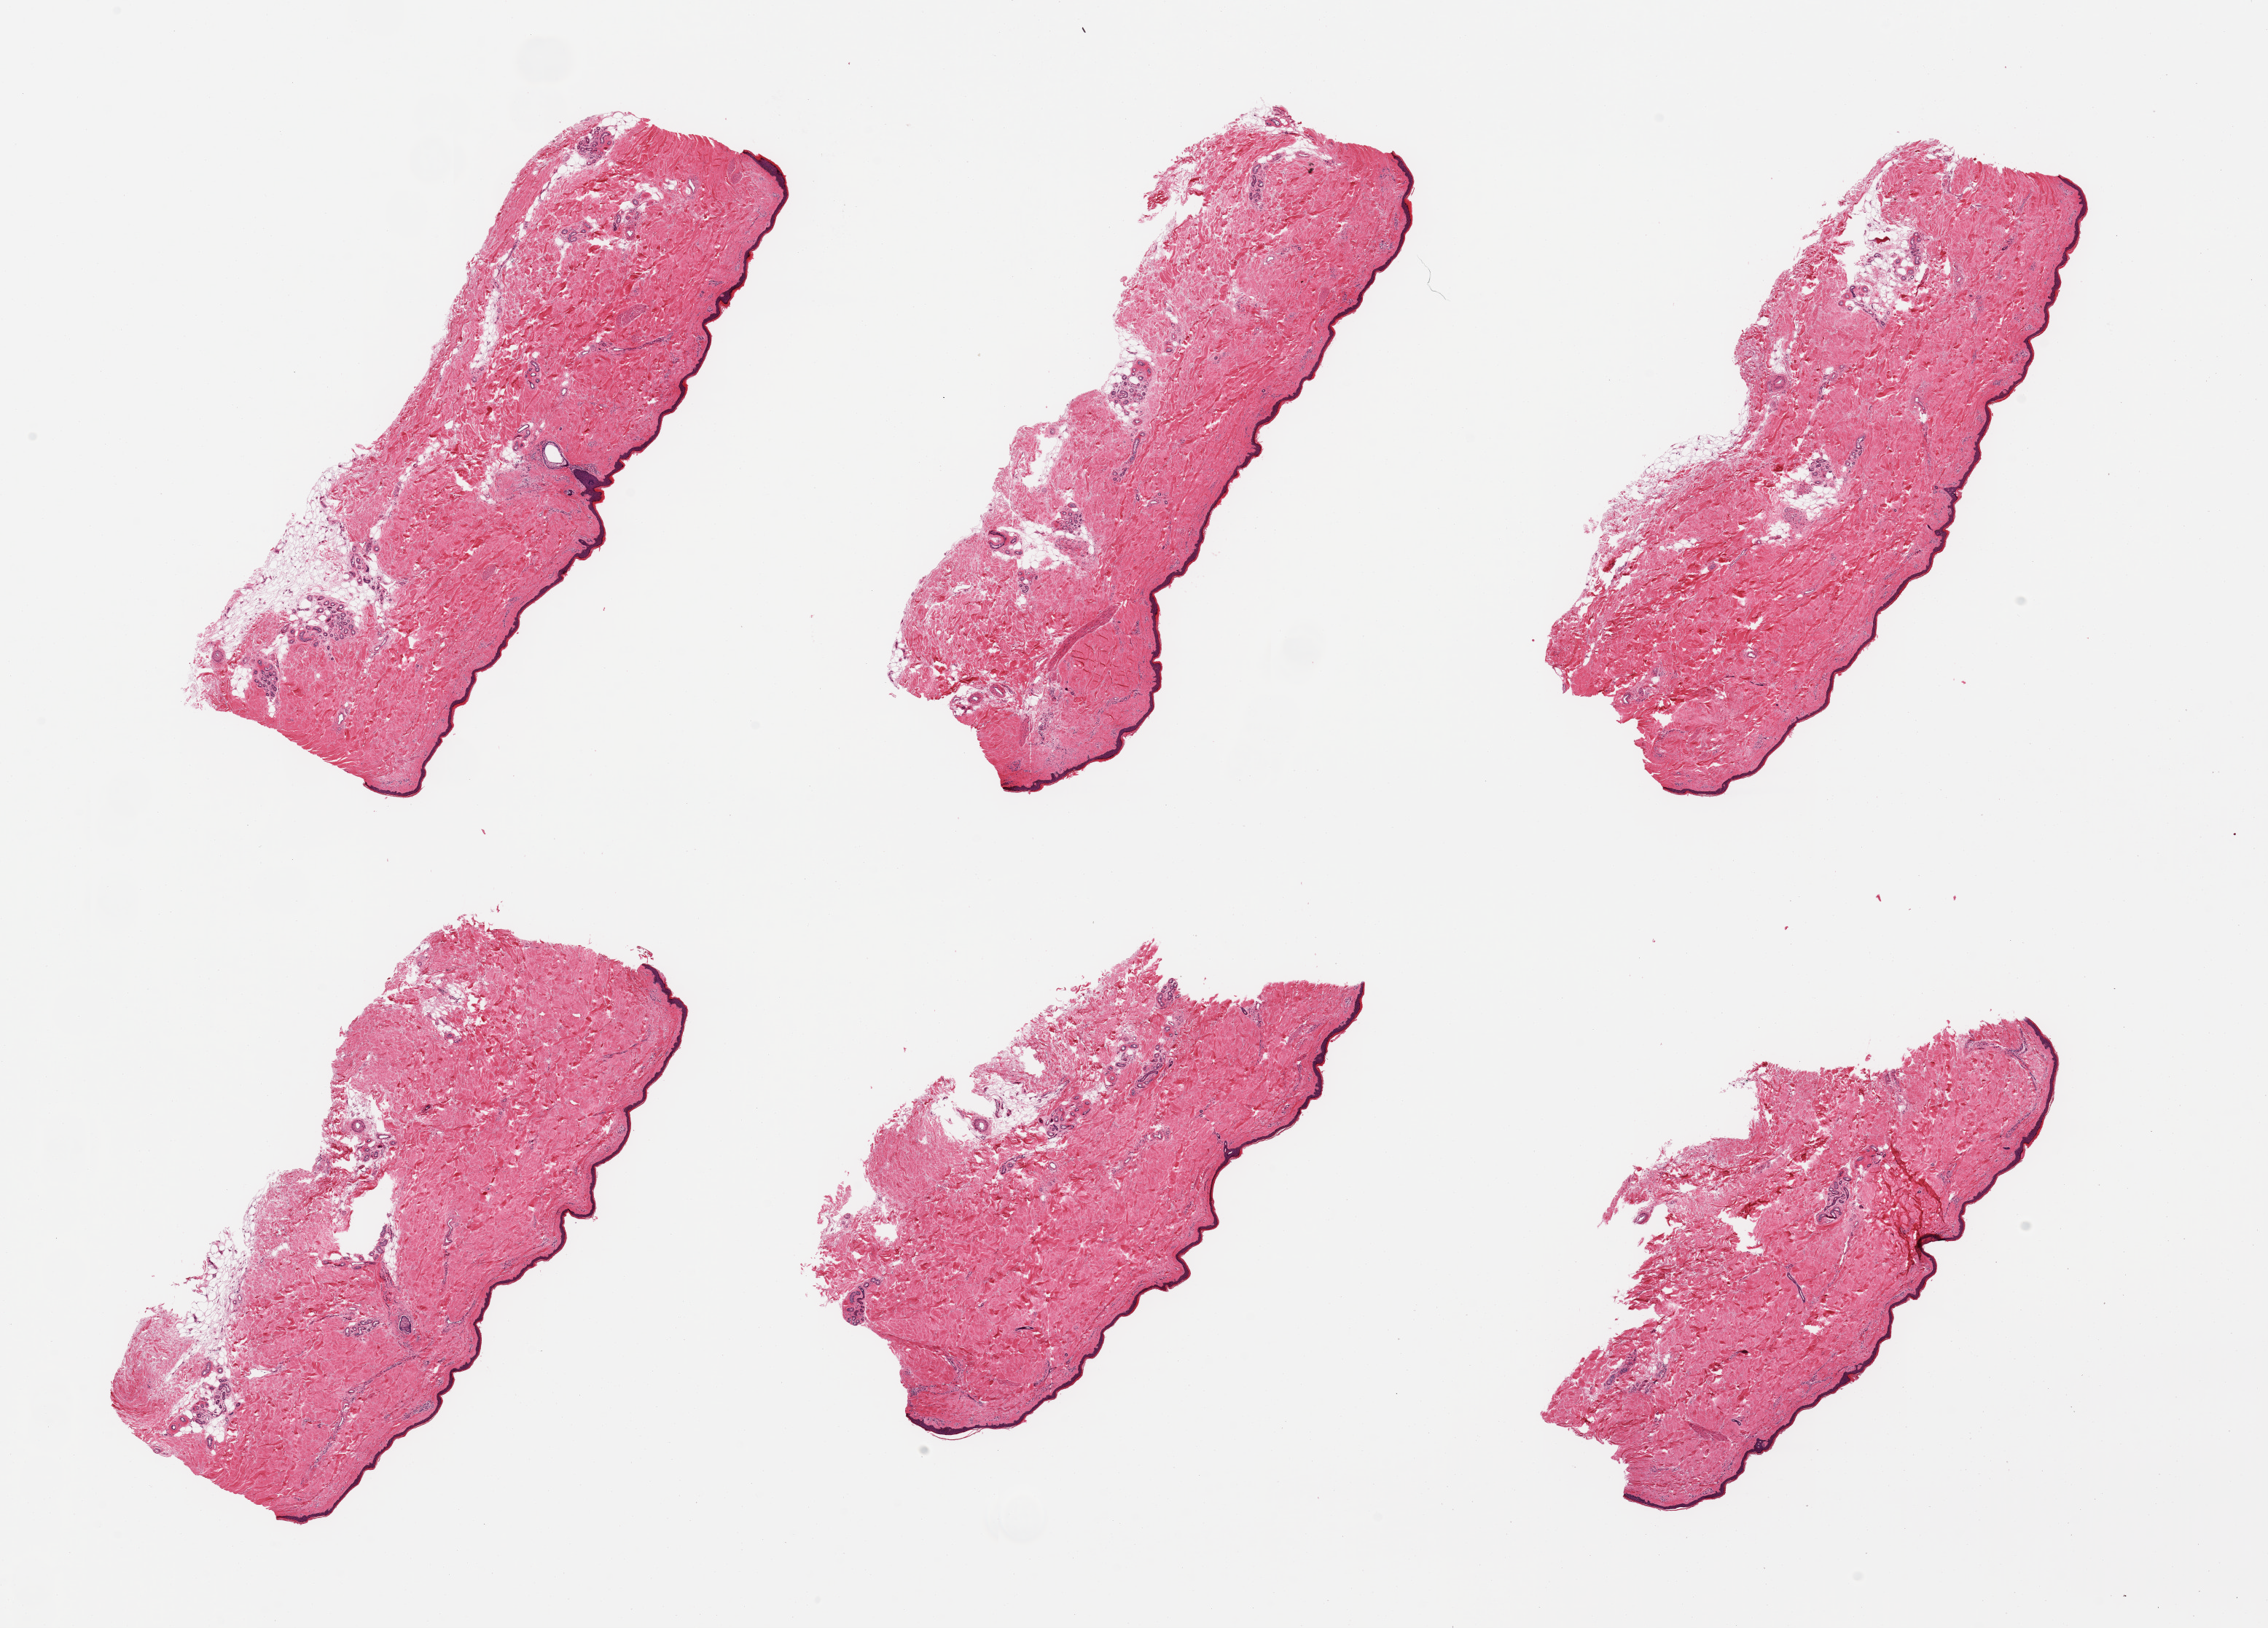
Whole-slide image, haematoxylin and eosin stain, brightfield, a low-resolution overview of the entire scanned area, about 24.6 x 17.7 mm (acquisition: 20x scan). PAXgene-fixed paraffin-embedded (PFPE) section. Sampled site (target tissue): skin of lower leg. Donor tissue sample. Donor: male.
Pathologist's review note for this sample: 6 pieces; ~10% internal/external fat, epidermis measures ~34 microns.